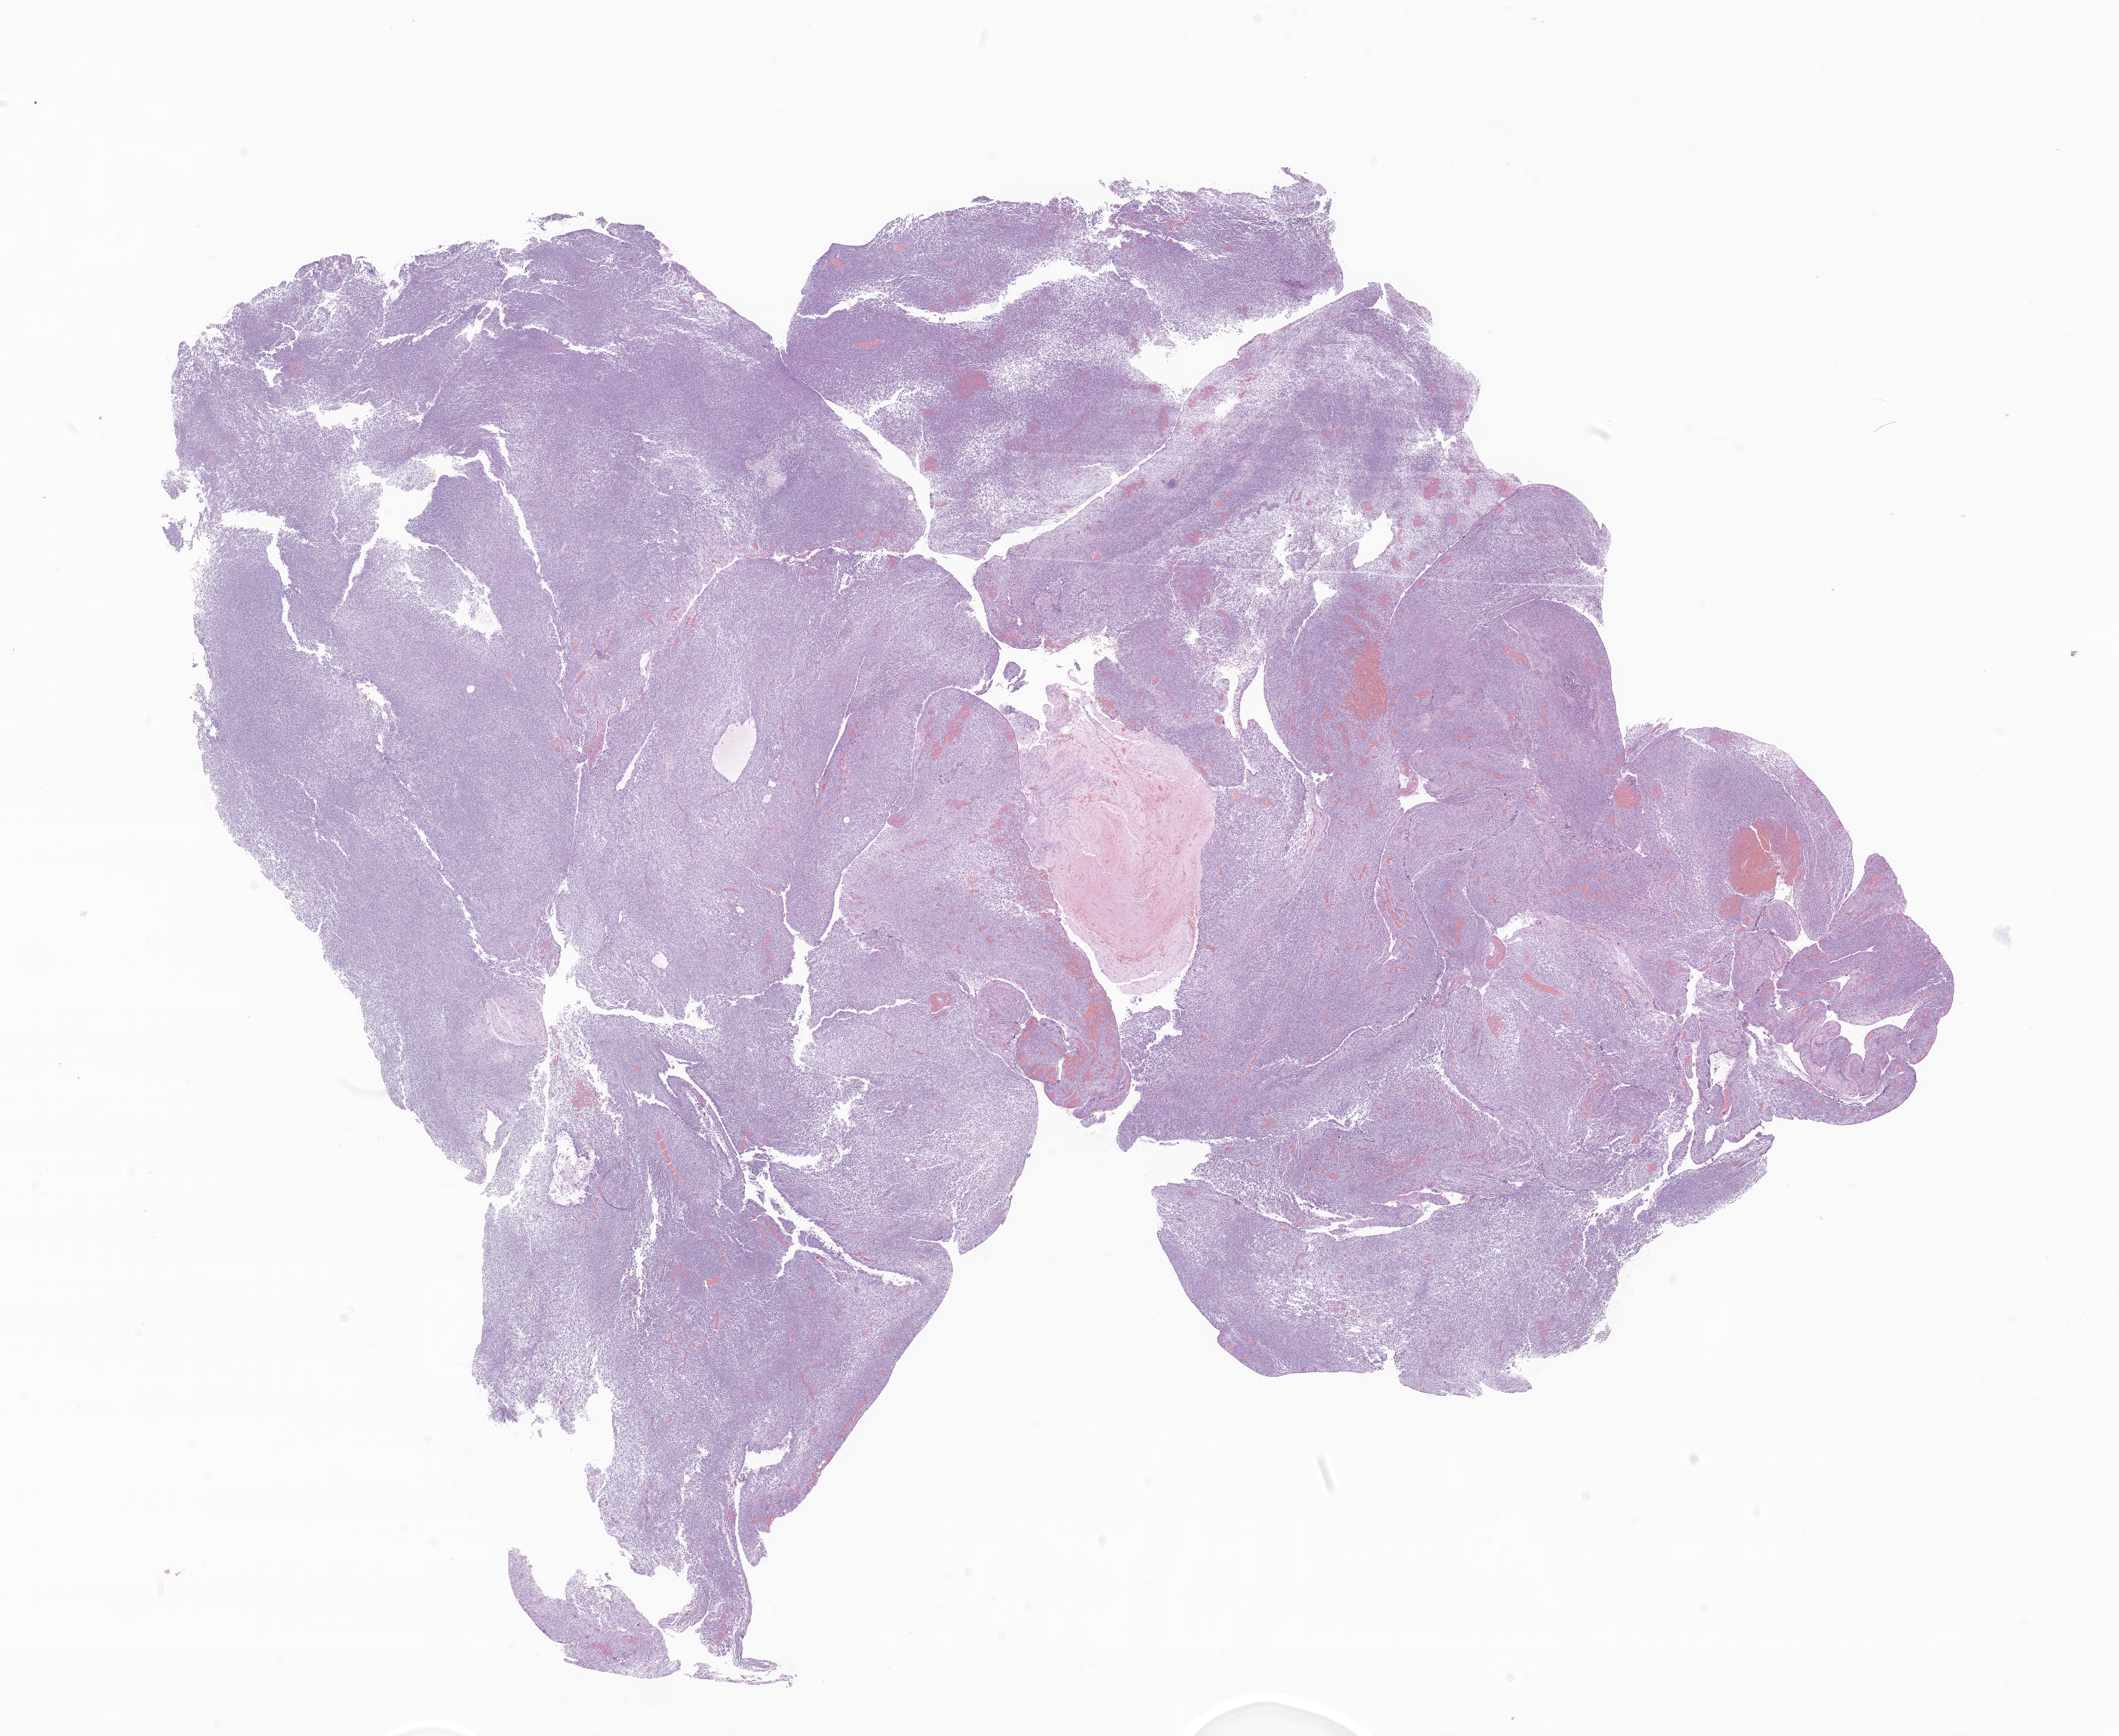
Digitized H&E-stained section of tumor tissue from the abdomen — whole scanned area (about 24.6 x 20.2 mm) shown as a low-resolution overview. Formalin-fixed, paraffin-embedded (FFPE) tissue. Female patient, age 539 days (about 1.5 years).
Diagnosis (ICD-O-3 morphology term): Neoplasm, uncertain whether benign or malignant.